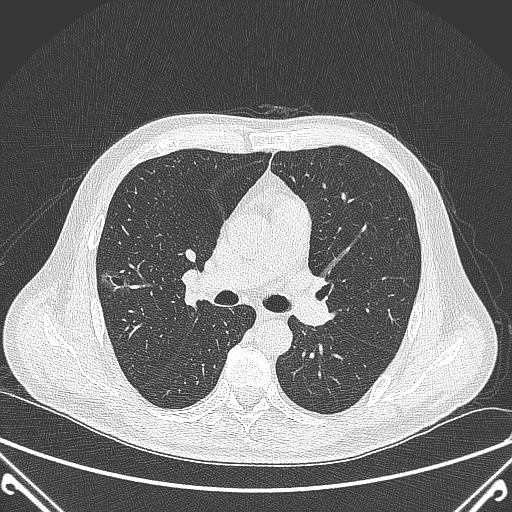
Chest CT, one axial slice; slice 222 of 360 in the series (ordered by position); 120 kVp; lung window (W 1500 / L -600 HU); 512 × 512 image matrix. Patient: male, 64 years. From the clinical record (not read from this slice): clinical TNM (as recorded): T1c N0 M0.
Outlined on this slice (bounding box drawn by a radiologist):
- lung tumour (recorded histology: adenocarcinoma): box from (x=95, y=249) to (x=142, y=309) px